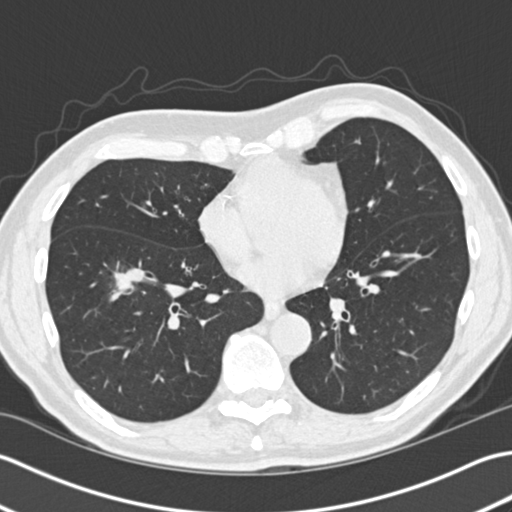
Low-dose screening chest CT, one axial slice; position 68 of 172 along the scan axis; reconstruction kernel B30f; 120 kVp; lung window (W 1500 / L -600 HU); 2 mm slice thickness; 512 × 512 image matrix.
Outlined on this slice (expert manual segmentation):
- lesion 1 (tumor, lower lobe of right lung): bounding box (x1, y1, x2, y2) in pixels: (114, 266, 146, 291)